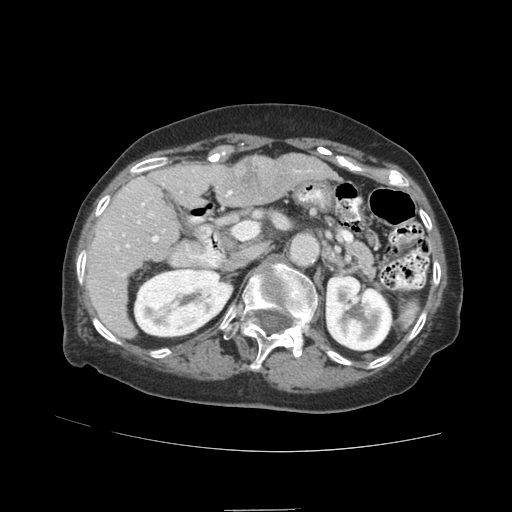
Contrast-enhanced abdominal CT (liver protocol), one axial slice; 140 kVp; soft-tissue window (W 400 / L 40 HU); 2.5 mm slice thickness; 512 × 512 image matrix, field of view 360 × 360 mm. Case-level facts recorded for this patient, not image findings: diagnosis: hepatocellular carcinoma (patient treated with transarterial chemoembolisation; whether this scan precedes or follows treatment is not stated here); TNM stage (as recorded): Stage-II; Child-Pugh class: A; tumour differentiation: moderately differentiated; tumour nodularity: multinodular.
Structures marked on this image (semi-automatic segmentation, software-assisted and operator-edited):
- liver parenchyma outside the tumour (the mass and vessels are separate outlines, so this box may not span the whole liver): box from (x=86, y=156) to (x=325, y=338) px
- mass: (x=233, y=156)–(x=284, y=204)
- liver vessels: (x=108, y=170)–(x=310, y=291)